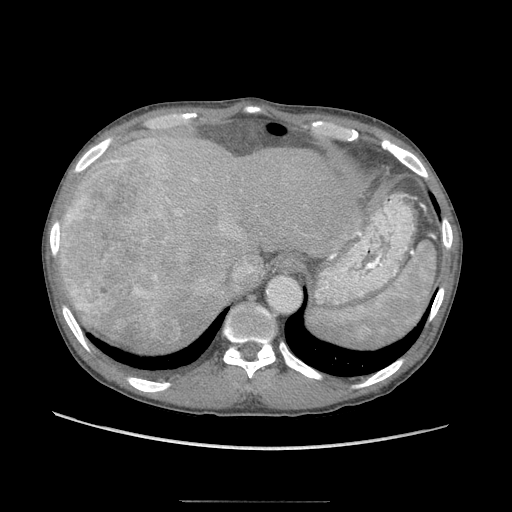
Contrast-enhanced abdominal CT (liver protocol), one axial slice. Position 76 of 103 along the scan axis. 120 kVp. Soft-tissue window (W 400 / L 40 HU). 2.5 mm slice thickness. 512 × 512 image matrix, field of view 380 × 380 mm. From the clinical record (not read from this slice): diagnosis: hepatocellular carcinoma (patient treated with transarterial chemoembolisation; whether this scan precedes or follows treatment is not stated here); TNM stage (as recorded): Stage-IIIA; Child-Pugh class: A; tumour nodularity: multinodular; tumour size: 16 cm.
Structures marked on this image (semi-automatically segmented with operator editing):
- liver parenchyma outside the tumour (the mass and vessels are separate outlines, so this box may not span the whole liver): bounding box (x1, y1, x2, y2) in pixels: (60, 131, 358, 346)
- mass: (62, 164, 189, 340)
- liver vessels: (149, 273, 265, 309)